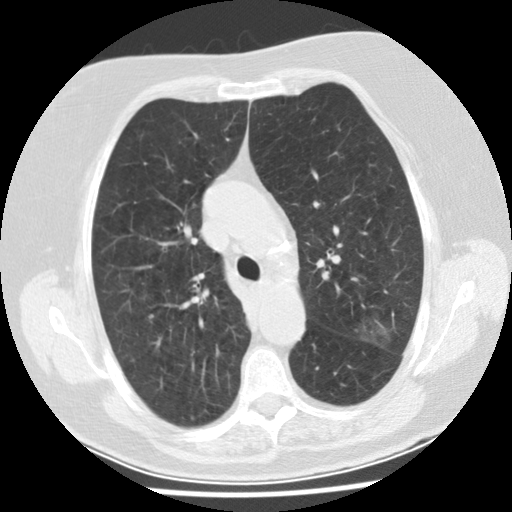
Chest CT (low-dose screening protocol), one axial image; baseline screening round; lung window (W 1500 / L -600 HU); 2.5 mm slice thickness; standard (soft-tissue) reconstruction kernel (STANDARD); slice 109 of 149 in the series; 512 × 512 image matrix, field of view 320 × 320 mm. Female, age 74 years at enrolment. Former smoker at enrolment.
Expert-annotated lung lesion, bounding box [x1, y1, x2, y2] px = [340, 304, 409, 359]. The screening reader recorded 2 non-calcified nodules or masses ≥4 mm on this exam; which of them this box marks is not recorded. Official screen result: positive, change unspecified: nodule(s) >= 4 mm or enlarging nodule(s), mass(es), or other non-specific abnormalities suspicious for lung cancer. Participant outcome: lung cancer diagnosed 532 days after this screen (after the second annual screen) — bronchiolo-alveolar adenocarcinoma, NOS, left upper lobe, stage IA (AJCC 6th edition), 20 mm at pathology.